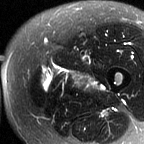
MRI of an extremity soft-tissue mass, one axial slice; position 15 of 60 along the scan axis; T2-weighted fat-saturated; MR volume resampled by the dataset authors to the PET/CT grid (not the native acquisition matrix); 3.27 mm slice thickness; 144 × 144 image matrix, field of view 141 × 141 mm. Female patient. From the clinical record (not read from this slice): histological type: pleiomorphic leiomyosarcoma; grade: intermediate; site of the primary tumour: left thigh.
Structures marked on this image (expert contour drawn on MRI and transferred to this co-registered scan by the dataset authors):
- gross tumour volume including surrounding oedema: box from (x=41, y=67) to (x=103, y=91) px